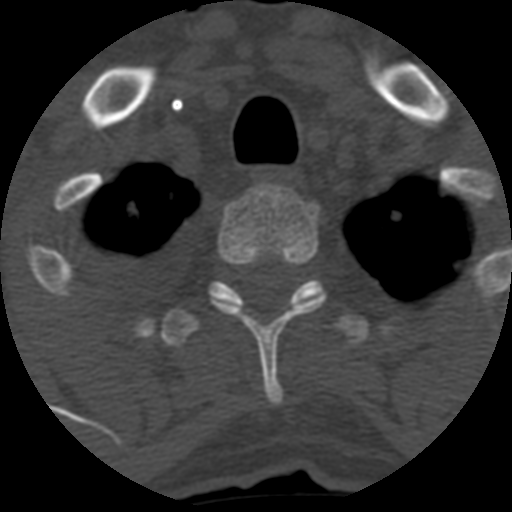
CT including the spine, one axial slice. Position 499 of 708 along the scan axis. Reconstruction kernel STANDARD. 120 kVp. One of 3 acquisitions stored at this slice position. Bone window (W 1800 / L 400 HU). 1.25 mm slice thickness. 512 × 512 image matrix, field of view 160 × 160 mm. Patient age 55 years. From the clinical record (not read from this slice): primary cancer: colon; vertebrae with lytic lesions (as recorded): T12, L1, L5.
Structures marked on this image (semi-automatic segmentation, software-assisted and operator-edited):
- T2 vertebra: box from (x=211, y=183) to (x=326, y=406) px
- T3 vertebra: (x=160, y=280)–(x=367, y=348)